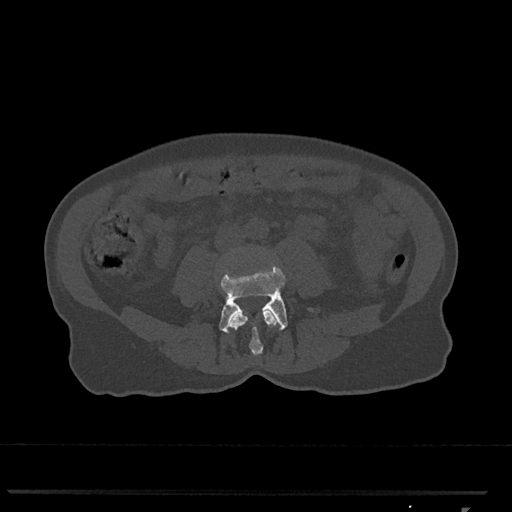
CT including the spine, one axial slice; slice 232 of 793 in the series (ordered by position); reconstruction kernel Br40s/3; 120 kVp; bone window (W 1800 / L 400 HU); 0.5 mm slice thickness; 512 × 512 image matrix. Patient: female, 62 years. From the clinical record (not read from this slice): primary cancer: renal.
Outlined on this slice (semi-automatically segmented with operator editing):
- L3 vertebra: box from (x=230, y=310) to (x=277, y=356) px
- L4 vertebra: (x=219, y=266)–(x=288, y=333)